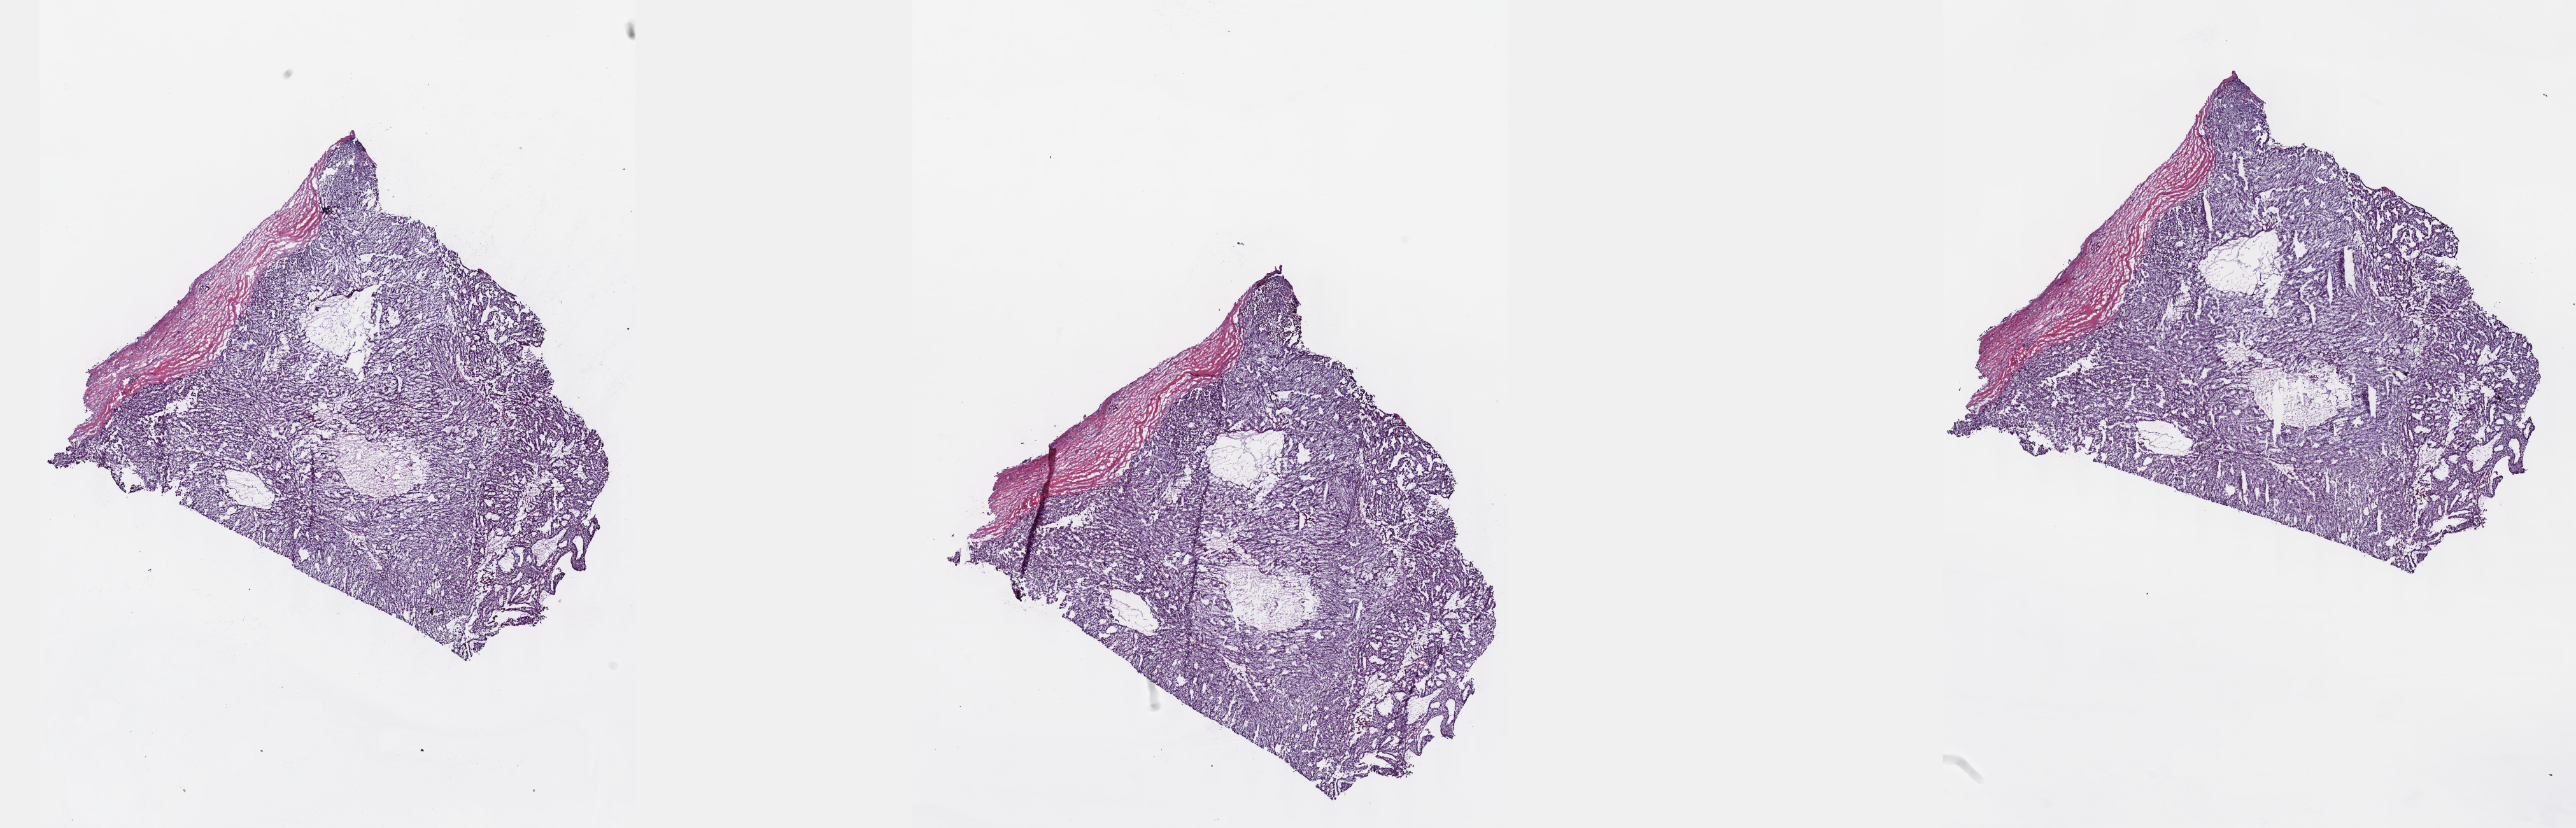
Whole-slide histology image, H&E-stained, whole scanned area (about 32.7 x 10.5 mm, slide scanned at 40x) shown as a low-resolution overview, frozen section, liver, primary tumour sample. Male patient; age at initial diagnosis 66 years. Histologic grade: G2 (moderately differentiated). Slide review estimates, as recorded: tumour cells 90%, tumour nuclei 80%, normal cells 10%, stromal cells 0%, necrosis 0%. Inflammatory infiltration, as recorded: lymphocyte infiltration 1%, monocyte infiltration 0%, neutrophil infiltration 0%.
AJCC pathologic stage: II (7th edition). Pathologic diagnosis: Hepatocellular carcinoma, NOS.